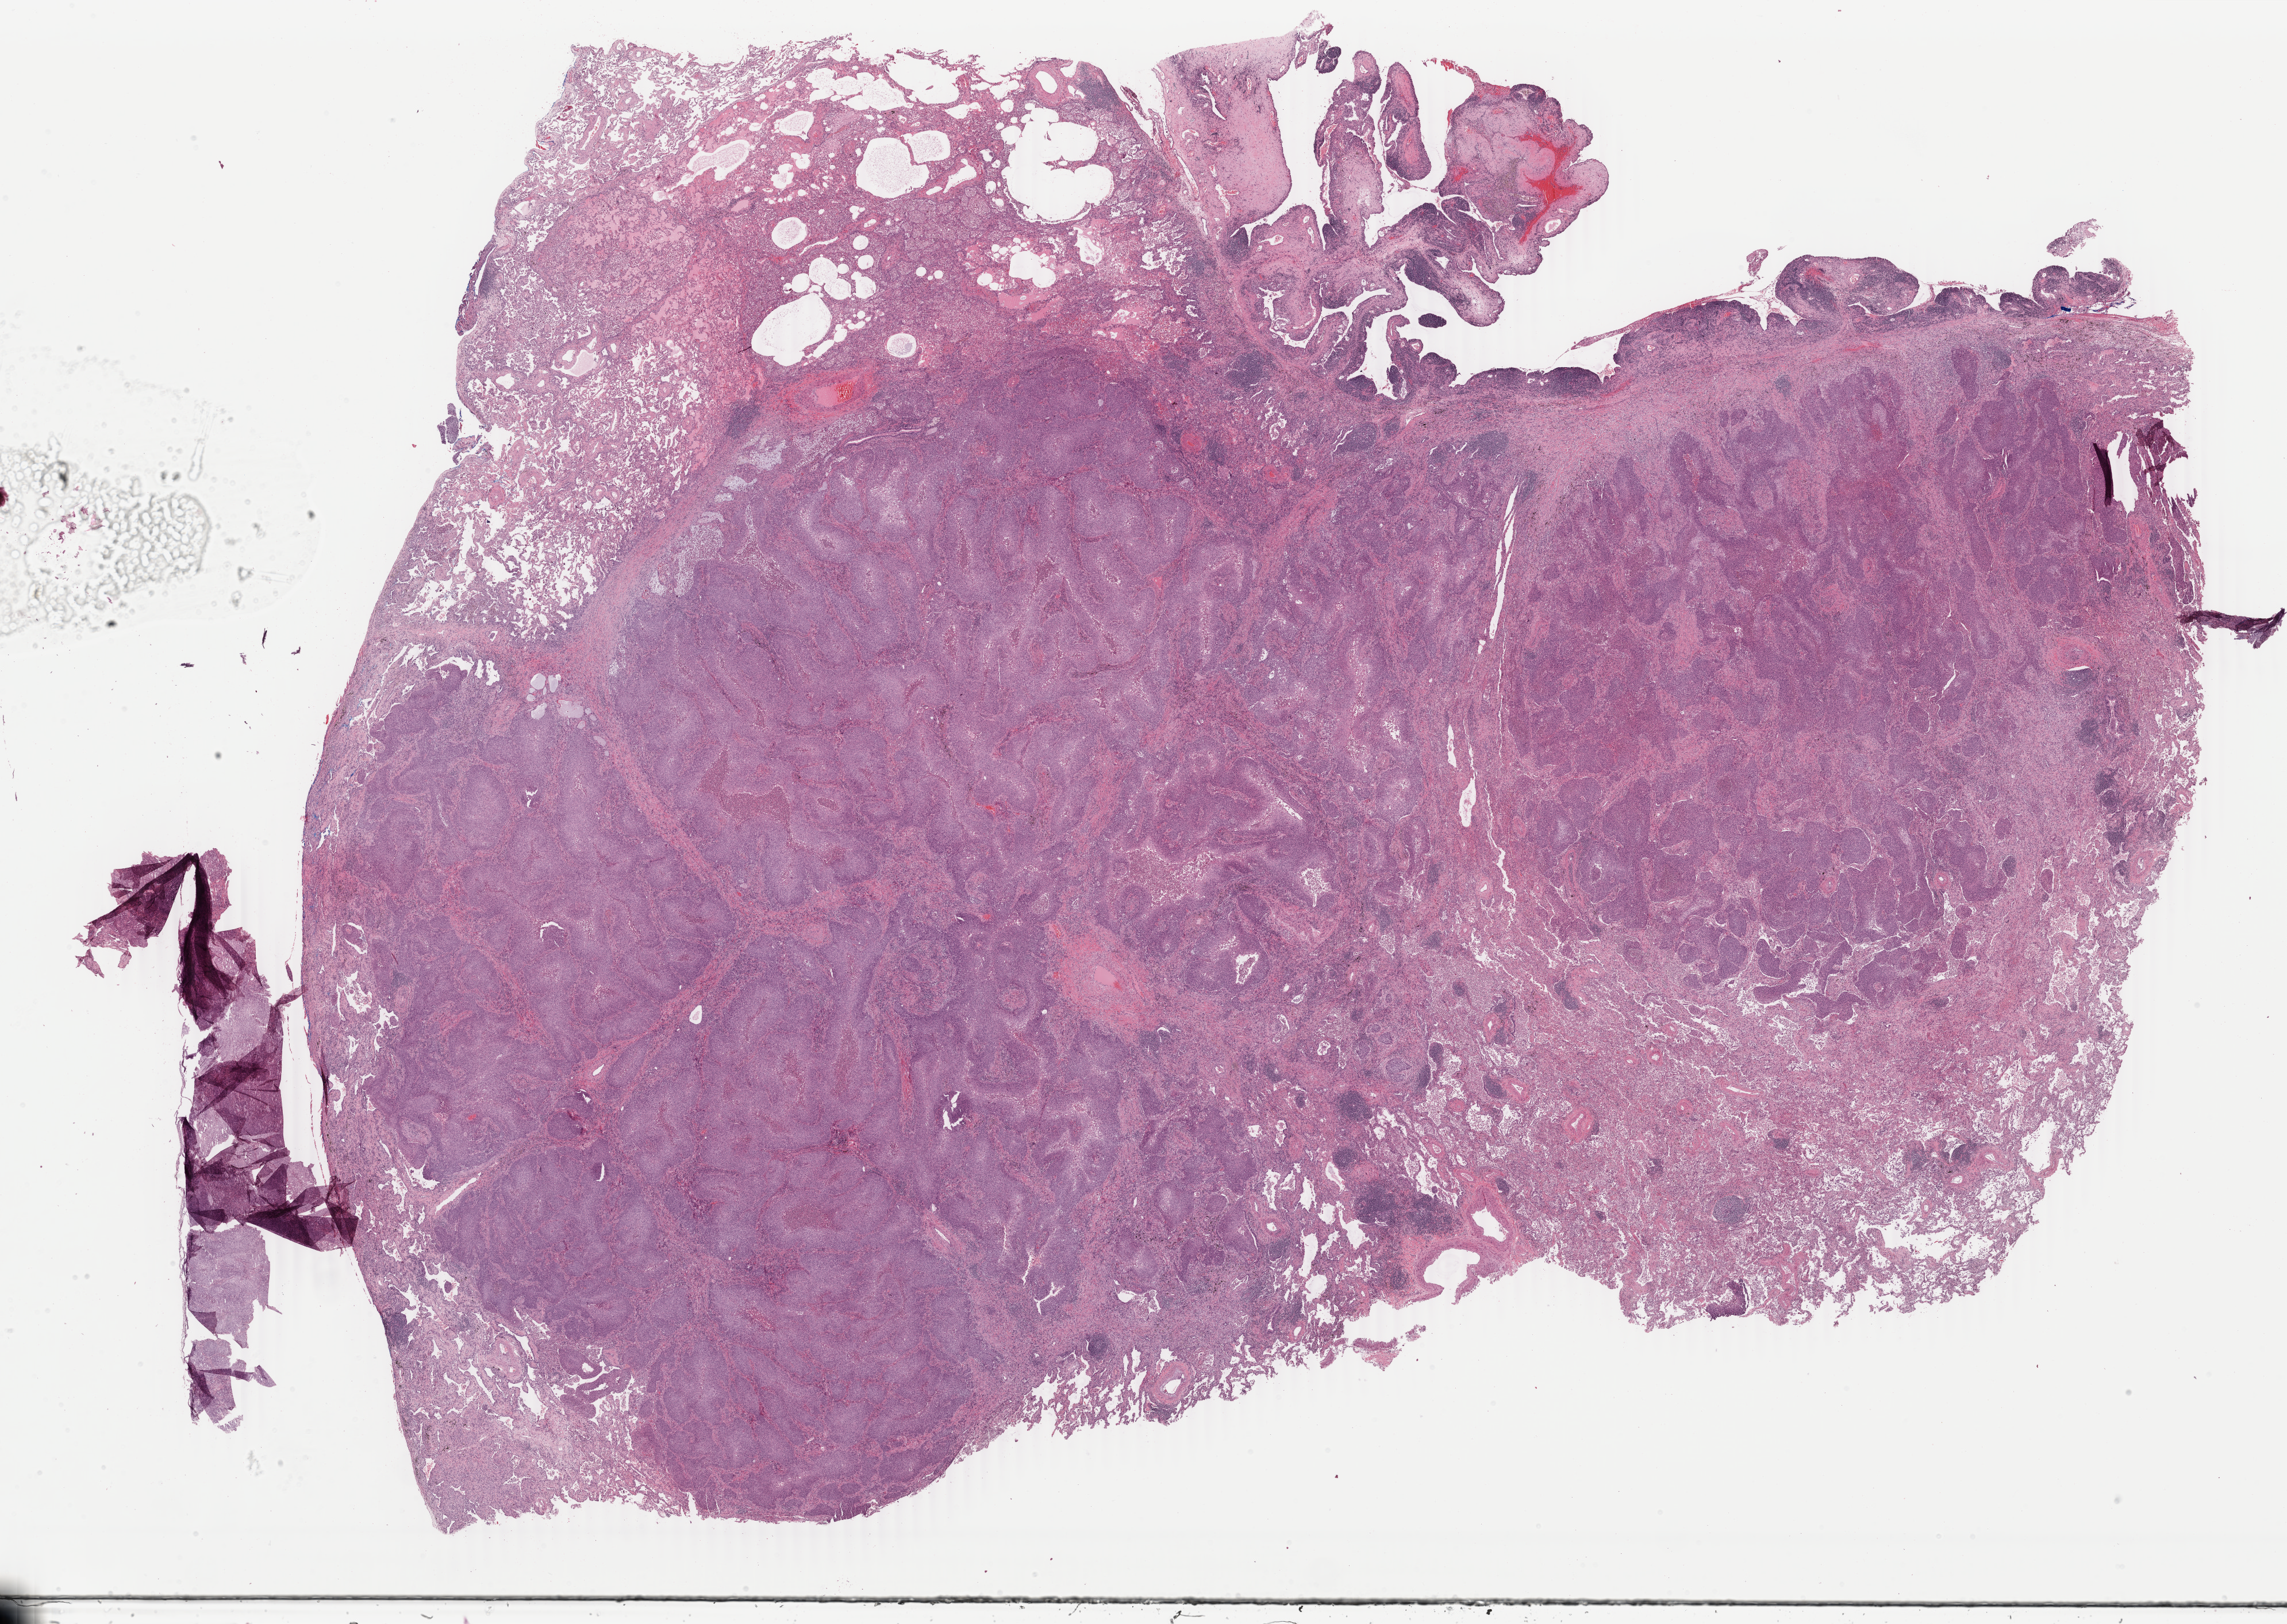
Digitized H&E-stained tissue section (whole slide), shown as a low-resolution overview of the whole scanned area (about 31.6 x 22.5 mm, slide scanned at 40x); formalin-fixed paraffin-embedded (FFPE) diagnostic section; lung, primary tumour sample. Female, age 62 years at initial diagnosis.
* pathologic diagnosis: Squamous cell carcinoma, NOS (lower lobe, lung)
* AJCC pathologic stage: IIIA (7th edition)